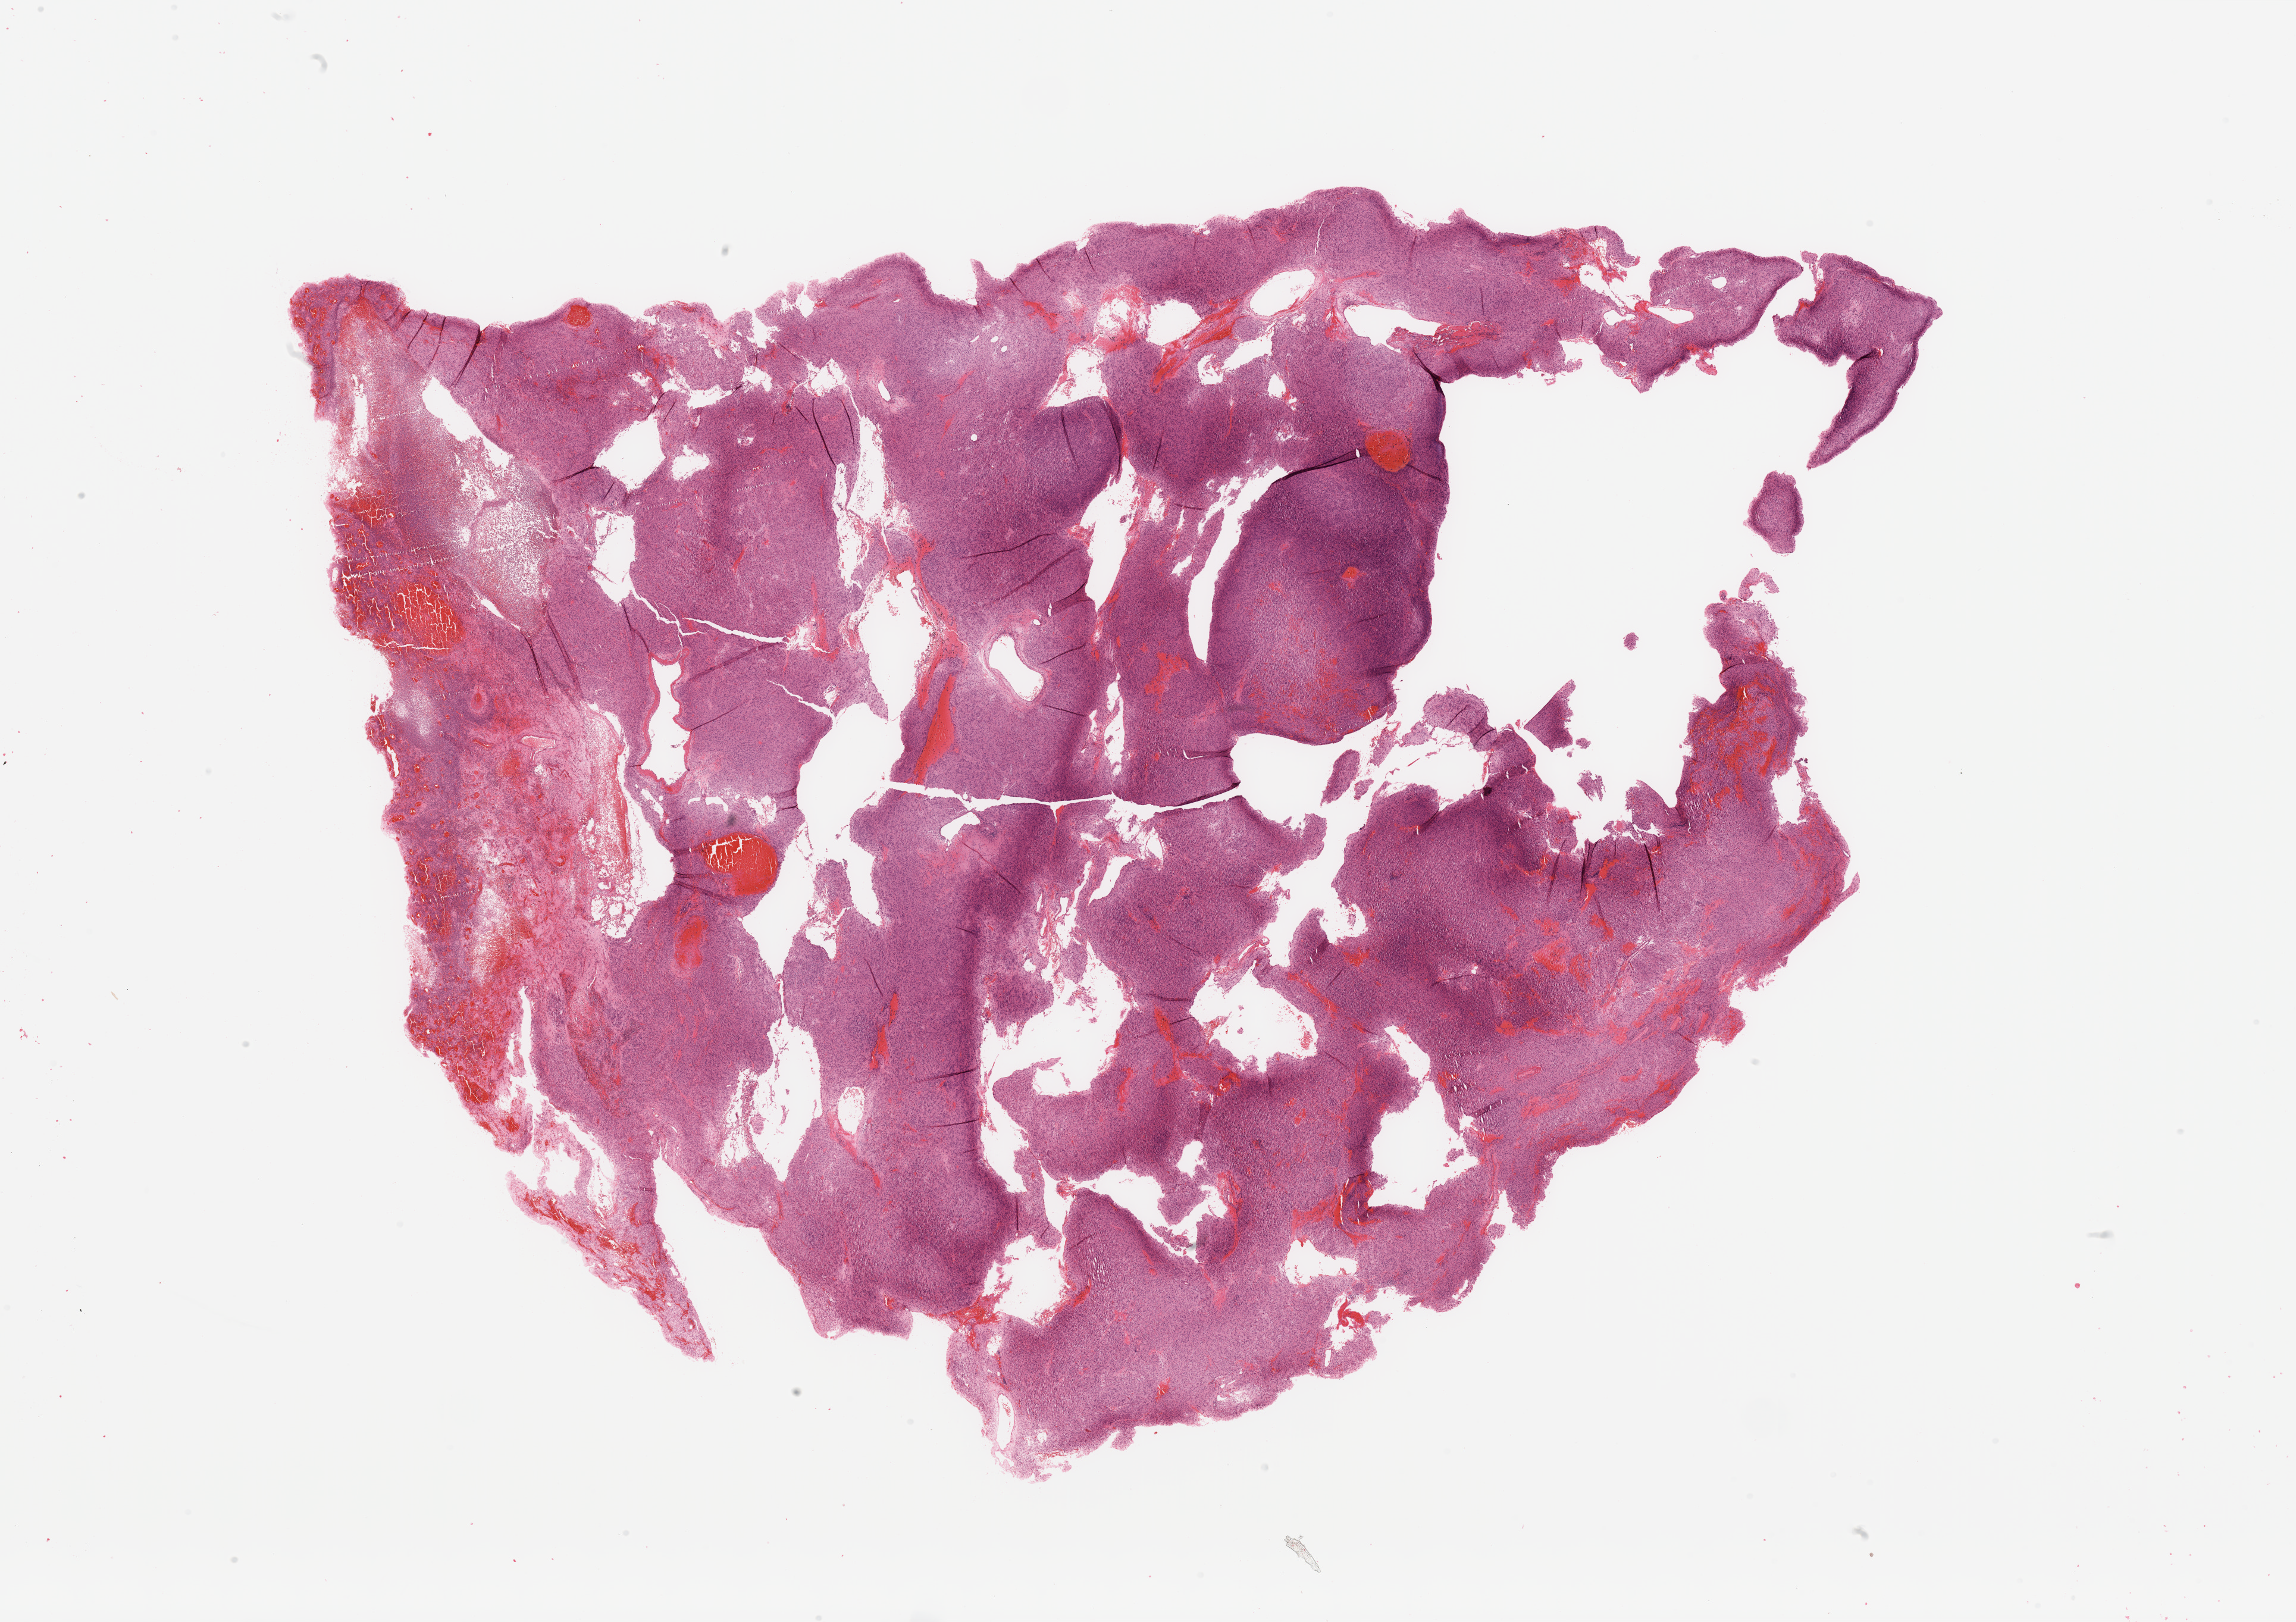
Digitized H&E tissue section (whole slide) — a low-resolution overview of the entire scanned area, about 30.5 x 21.6 mm (from a 20x scan). Patient: female, age 73 years.
Patient diagnosis (cohort enrolment): sarcoma (site not recorded at cohort level).